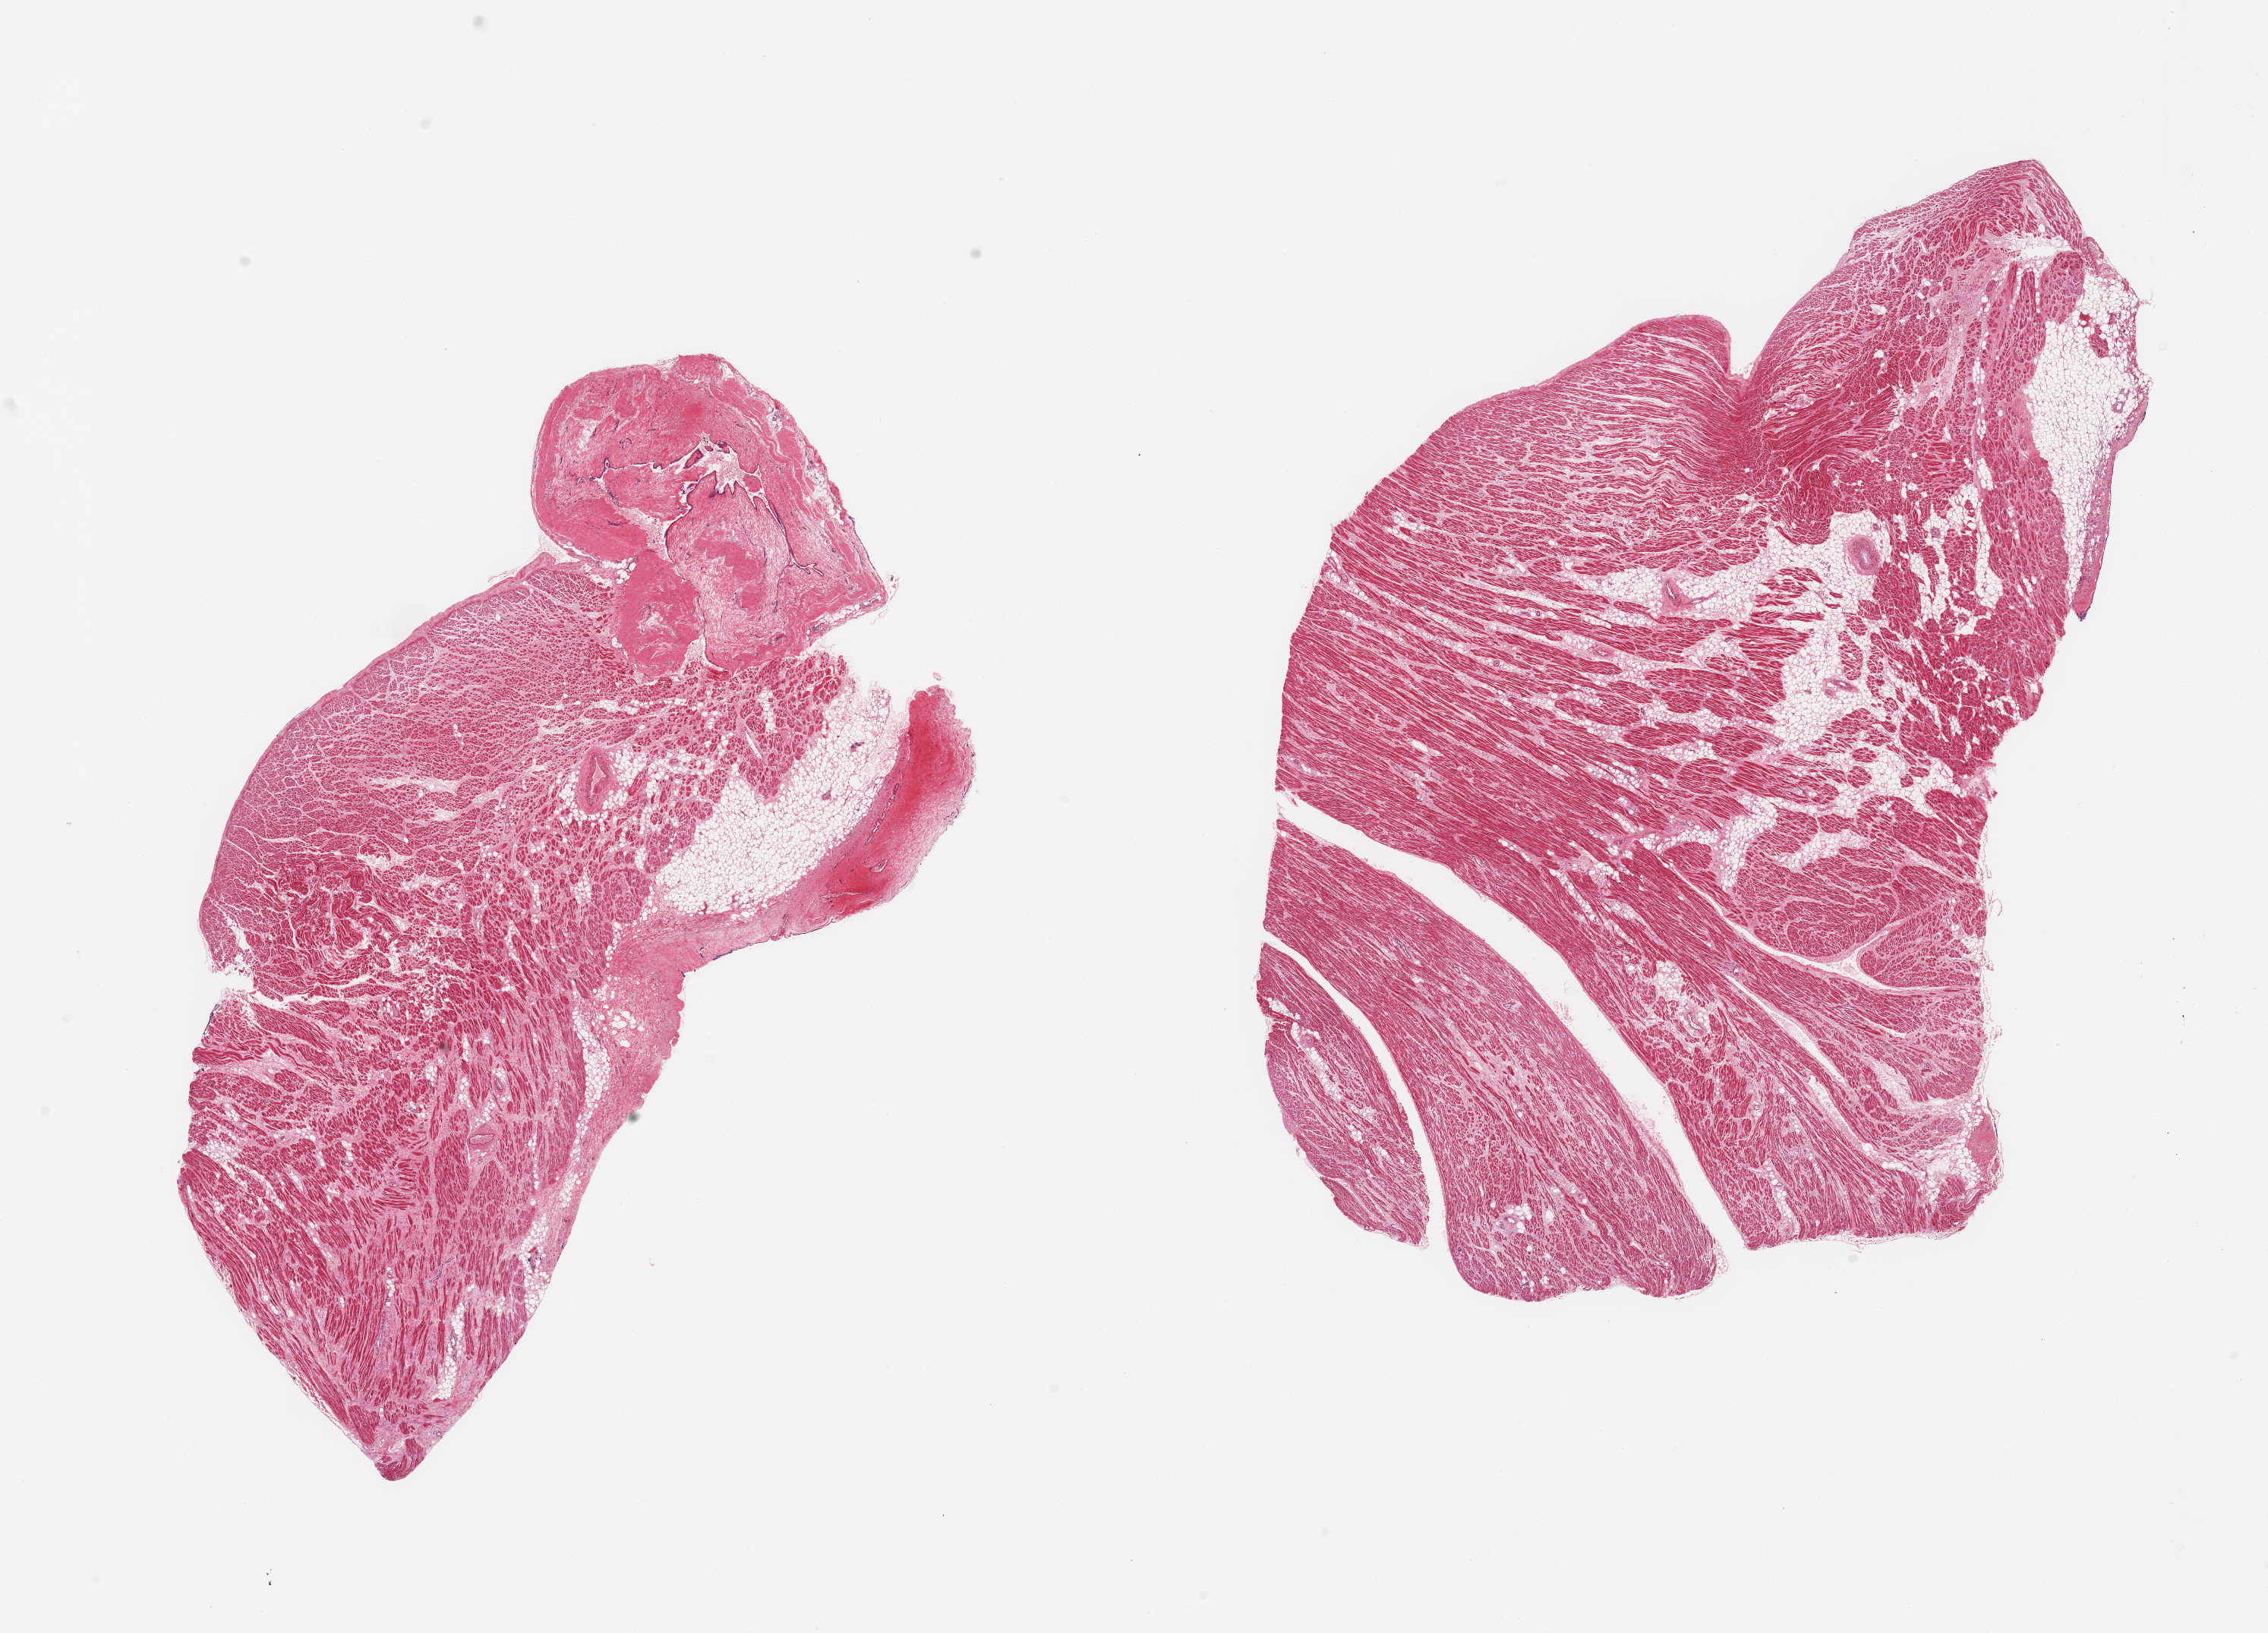
Digitized hematoxylin and eosin (H&E)-stained section — a low-resolution overview of the entire scanned area, about 23.6 x 17.0 mm (slide scanned at 20x); PAXgene-fixed paraffin-embedded (PFPE) section; section of auricular appendage (target tissue); donor tissue sample. Donor sex: male.
• review note (as recorded): 2 pieces, no abnormalities